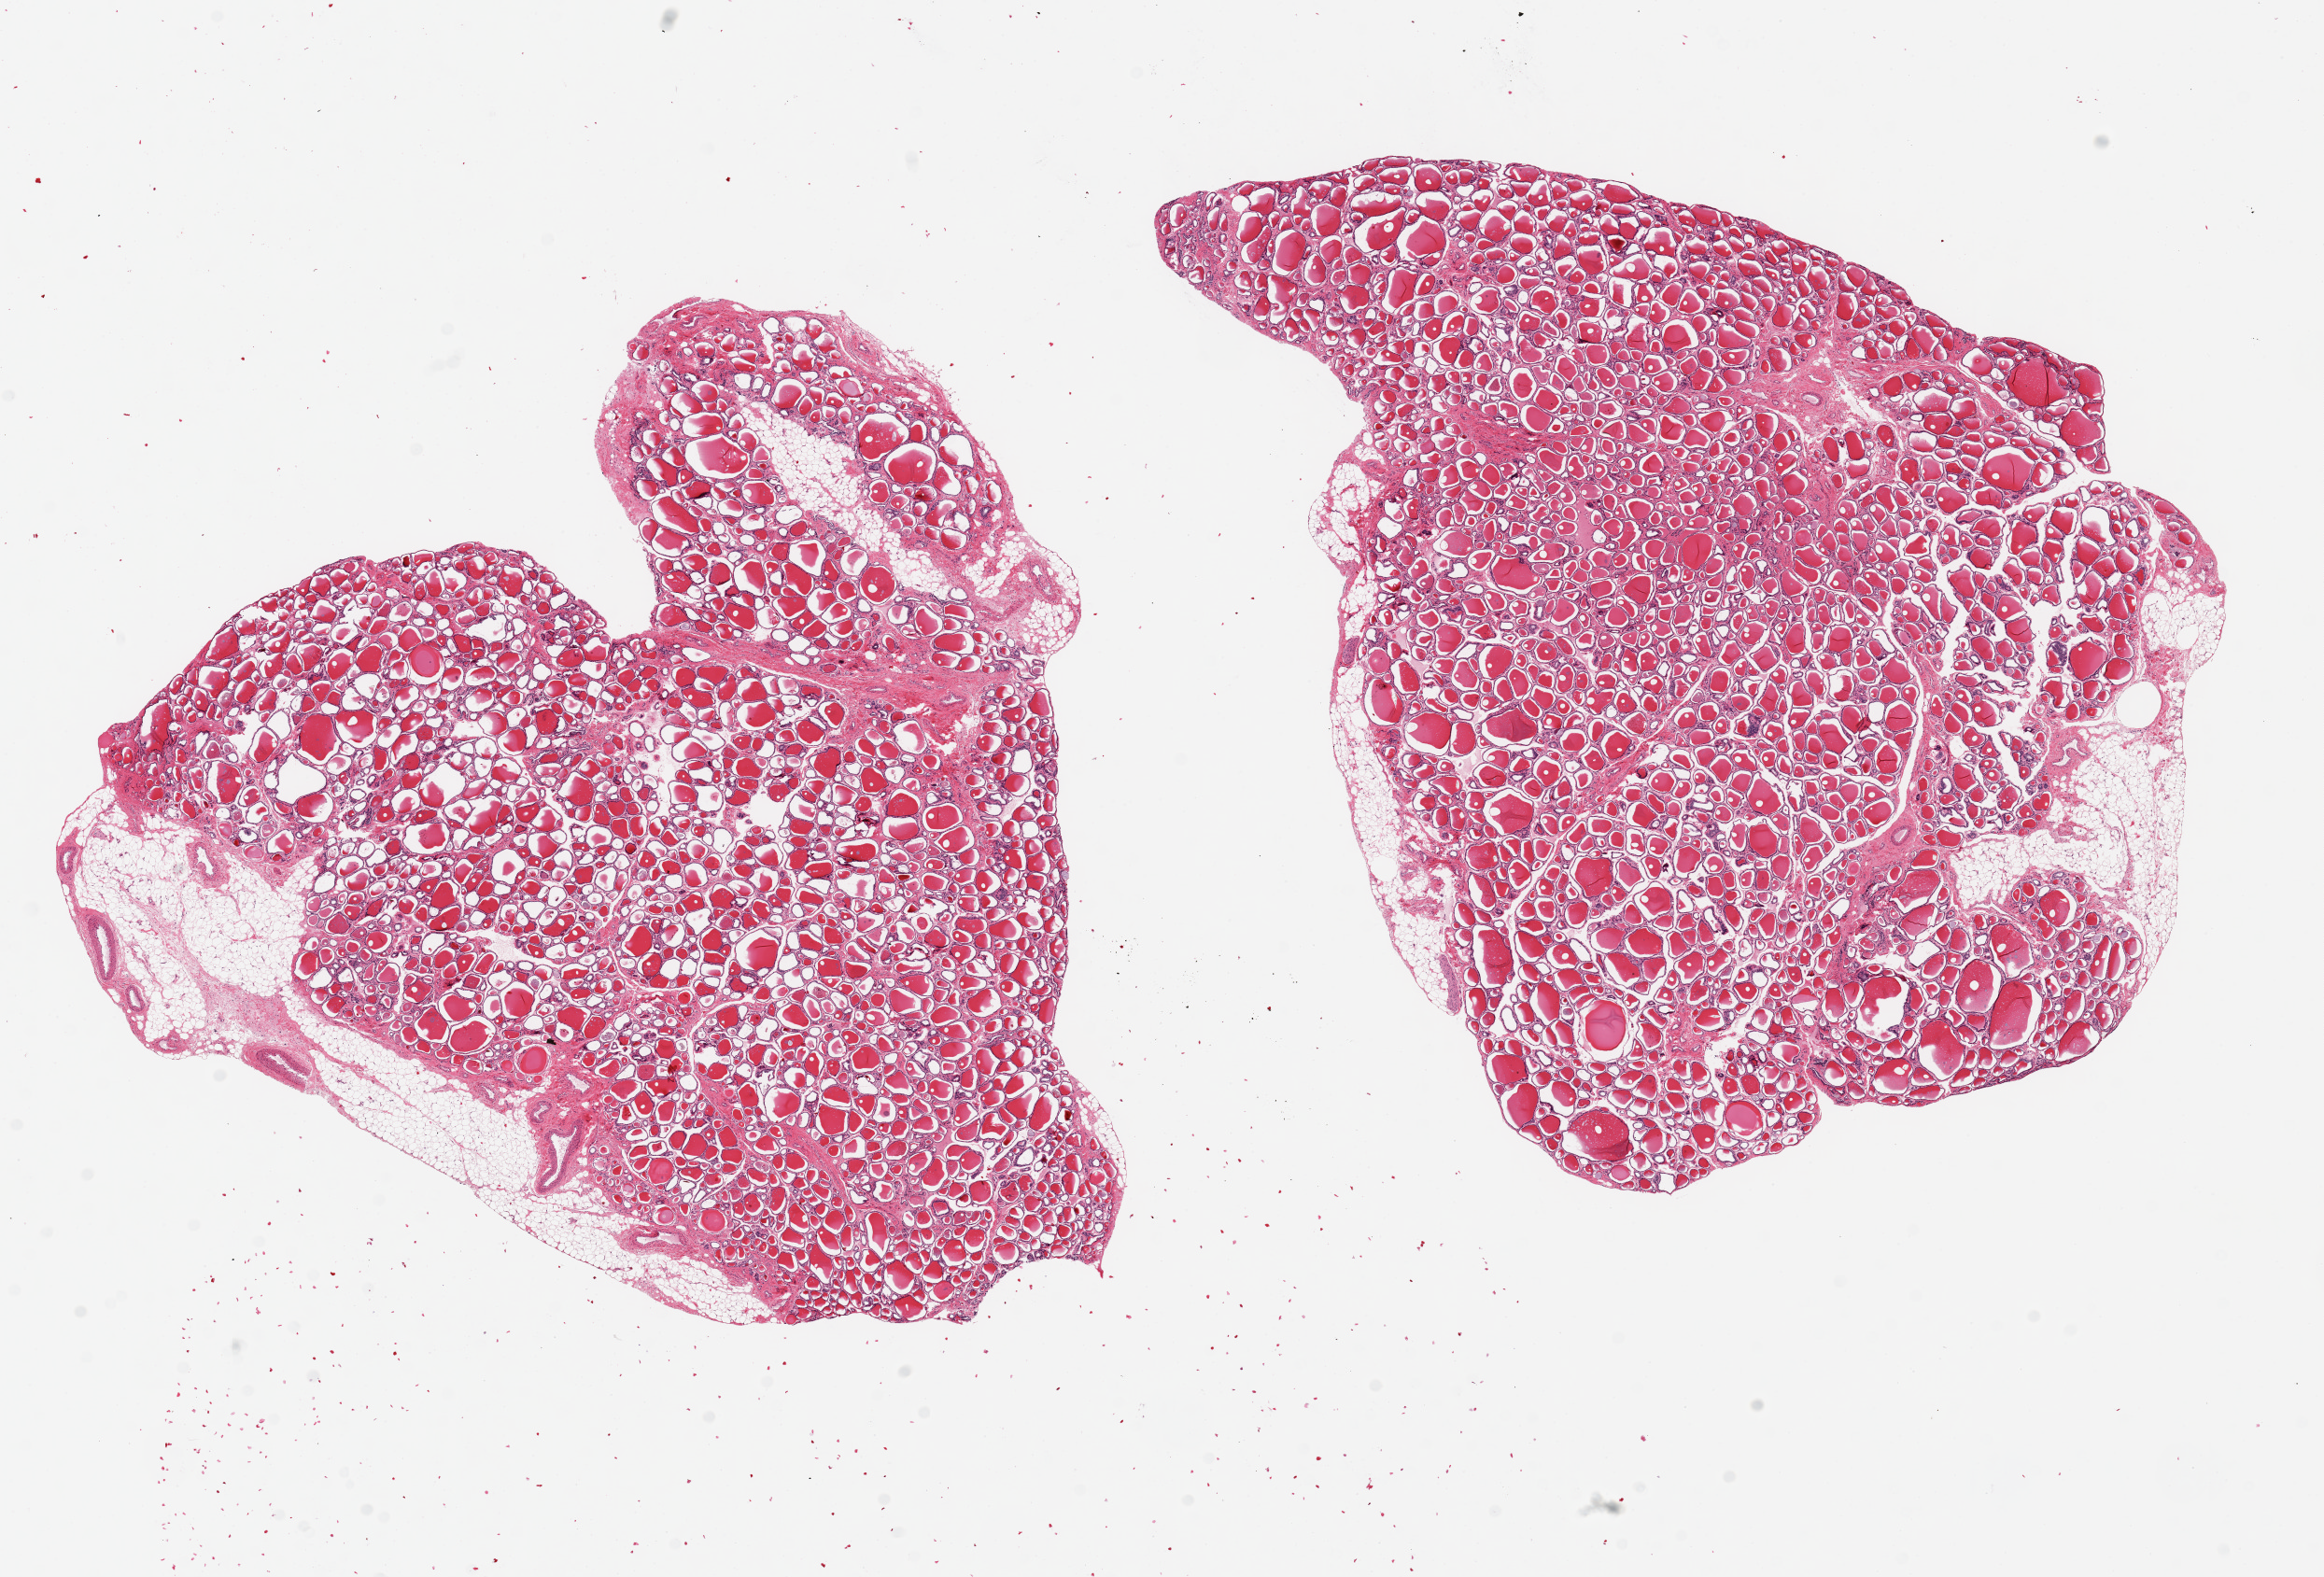
Digitized H&E-stained section — shown as a low-resolution overview of the whole scanned area (about 19.7 x 13.4 mm); PAXgene-fixed, paraffin-embedded tissue; target tissue: thyroid; tissue donor sample. Male donor.
Review note (as recorded): 2 pieces, 9.5x9 & 9x8mm; 10% peripheral adipose.